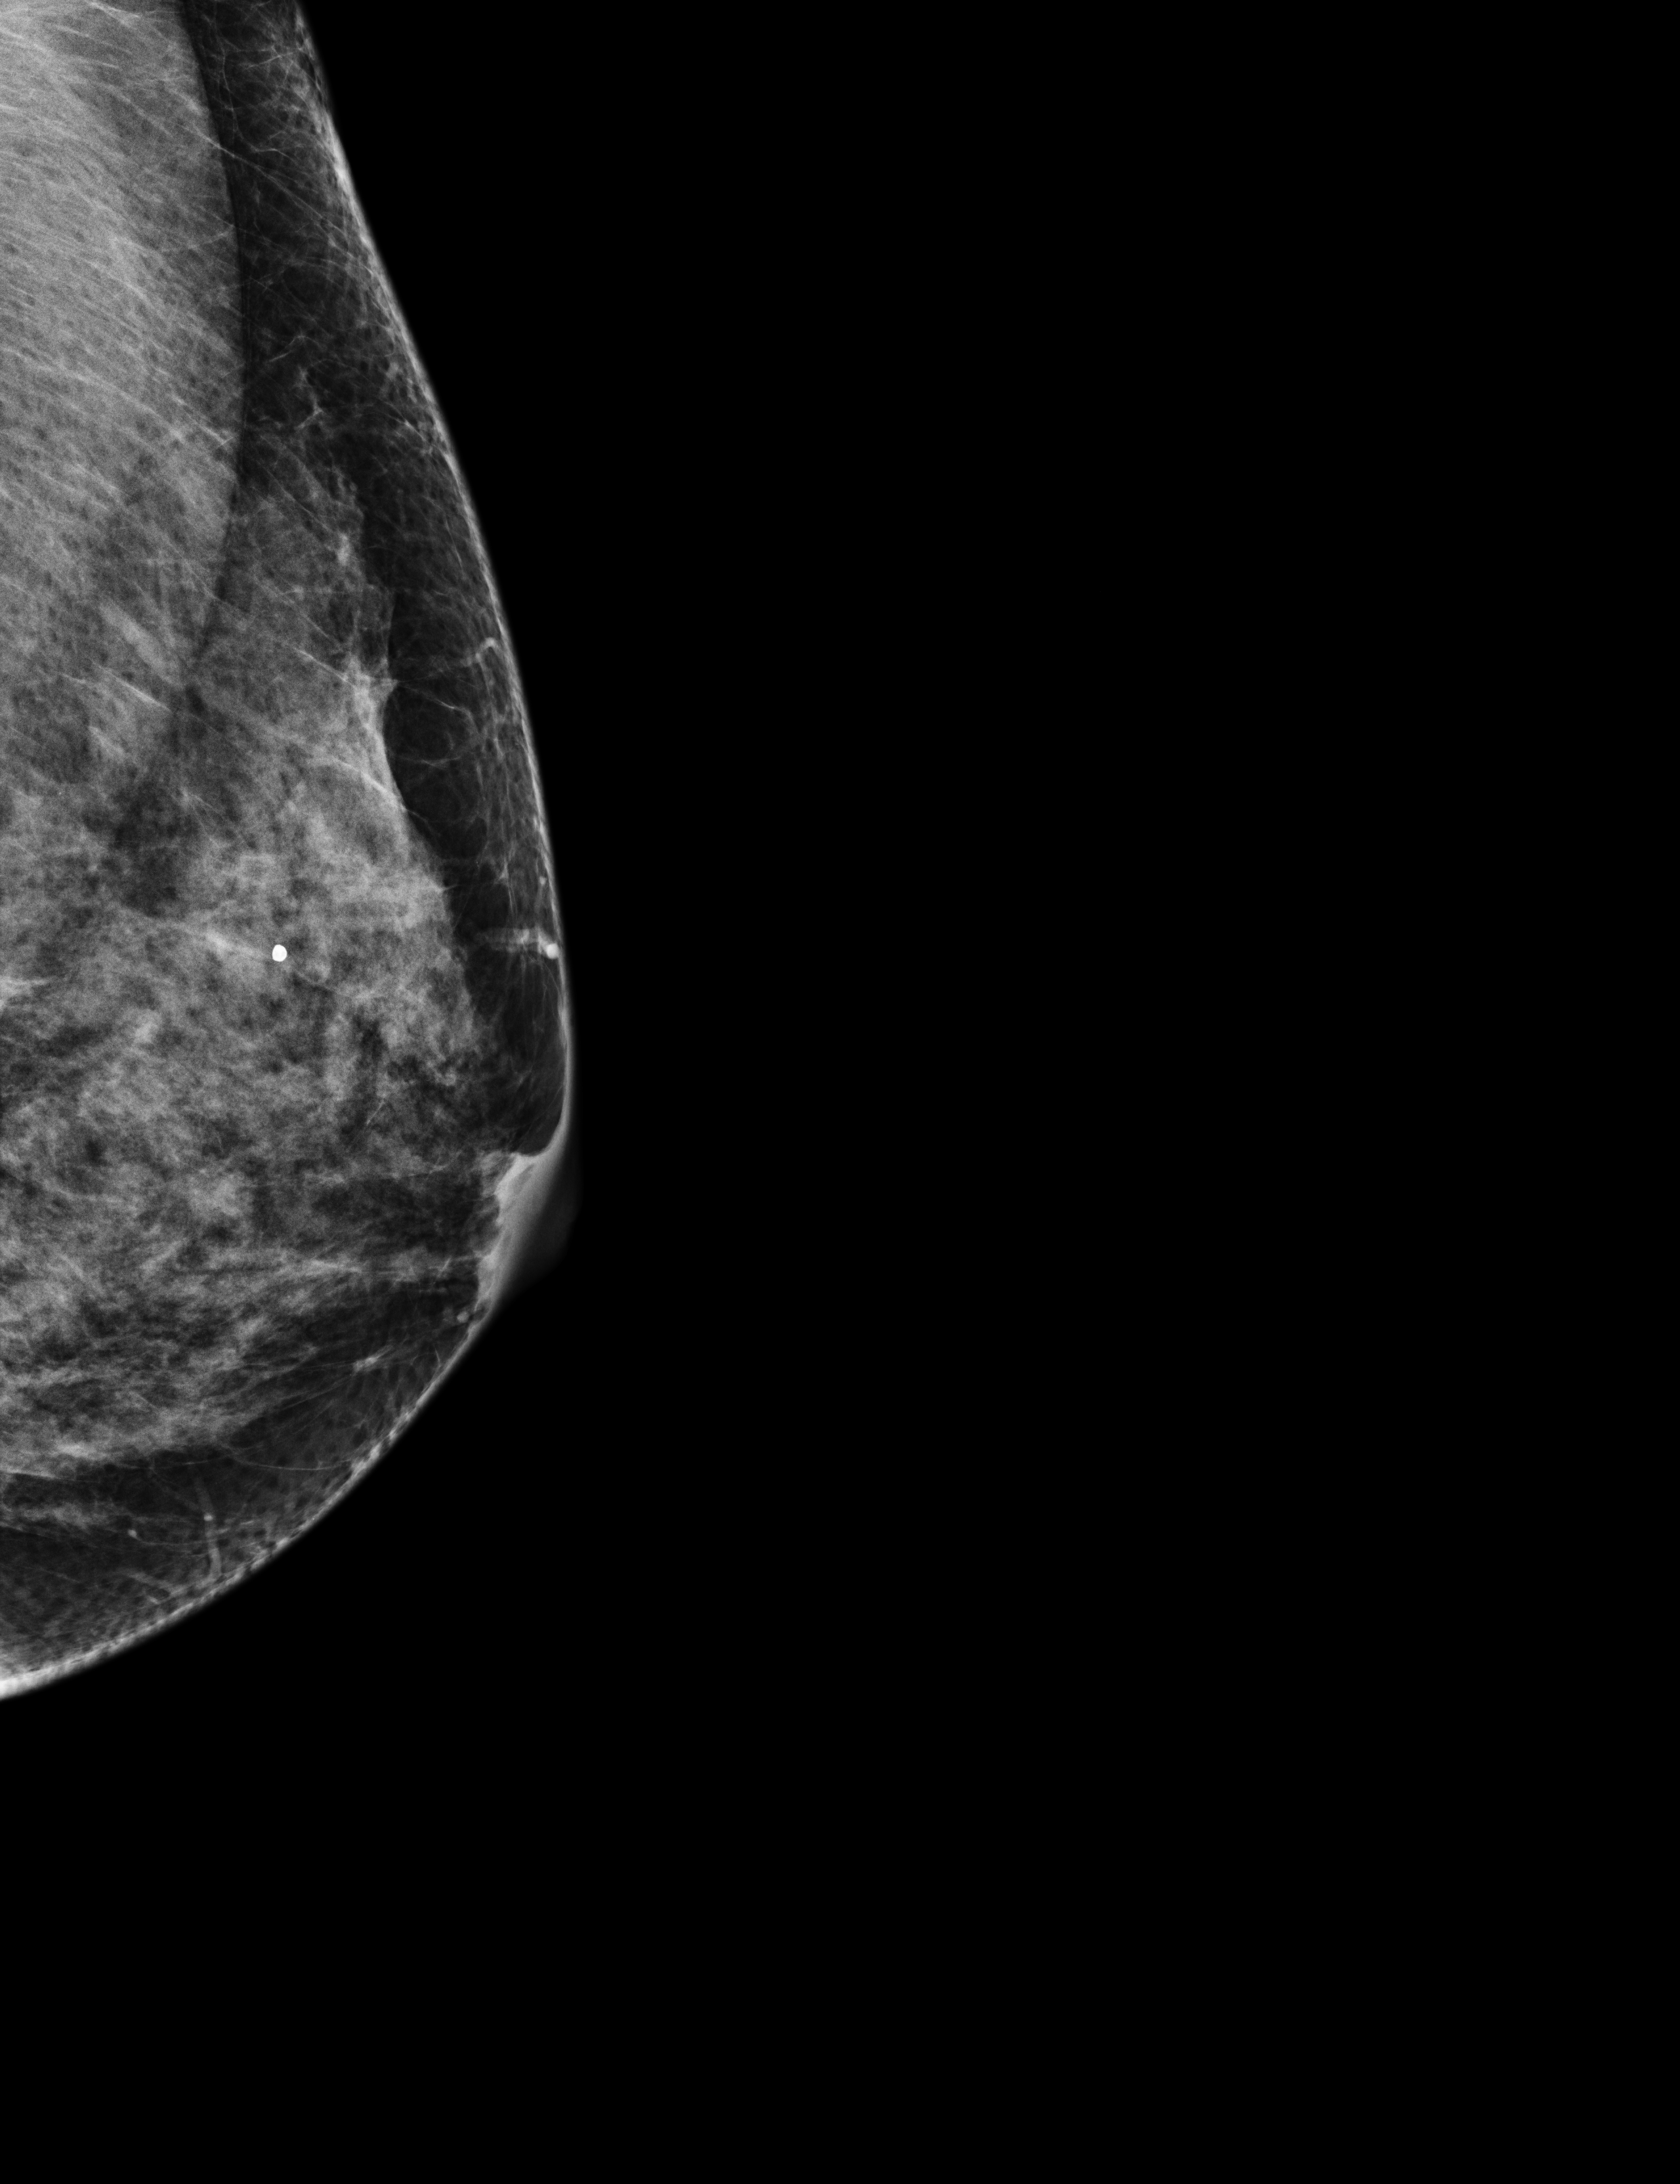
Annual screening mammography examination, system: Selenia Dimensions. Patient aged 41 years (female).
Image type: full-field digital mammogram. Breast: left. Projection: laterally exaggerated craniocaudal (XCCL) view.